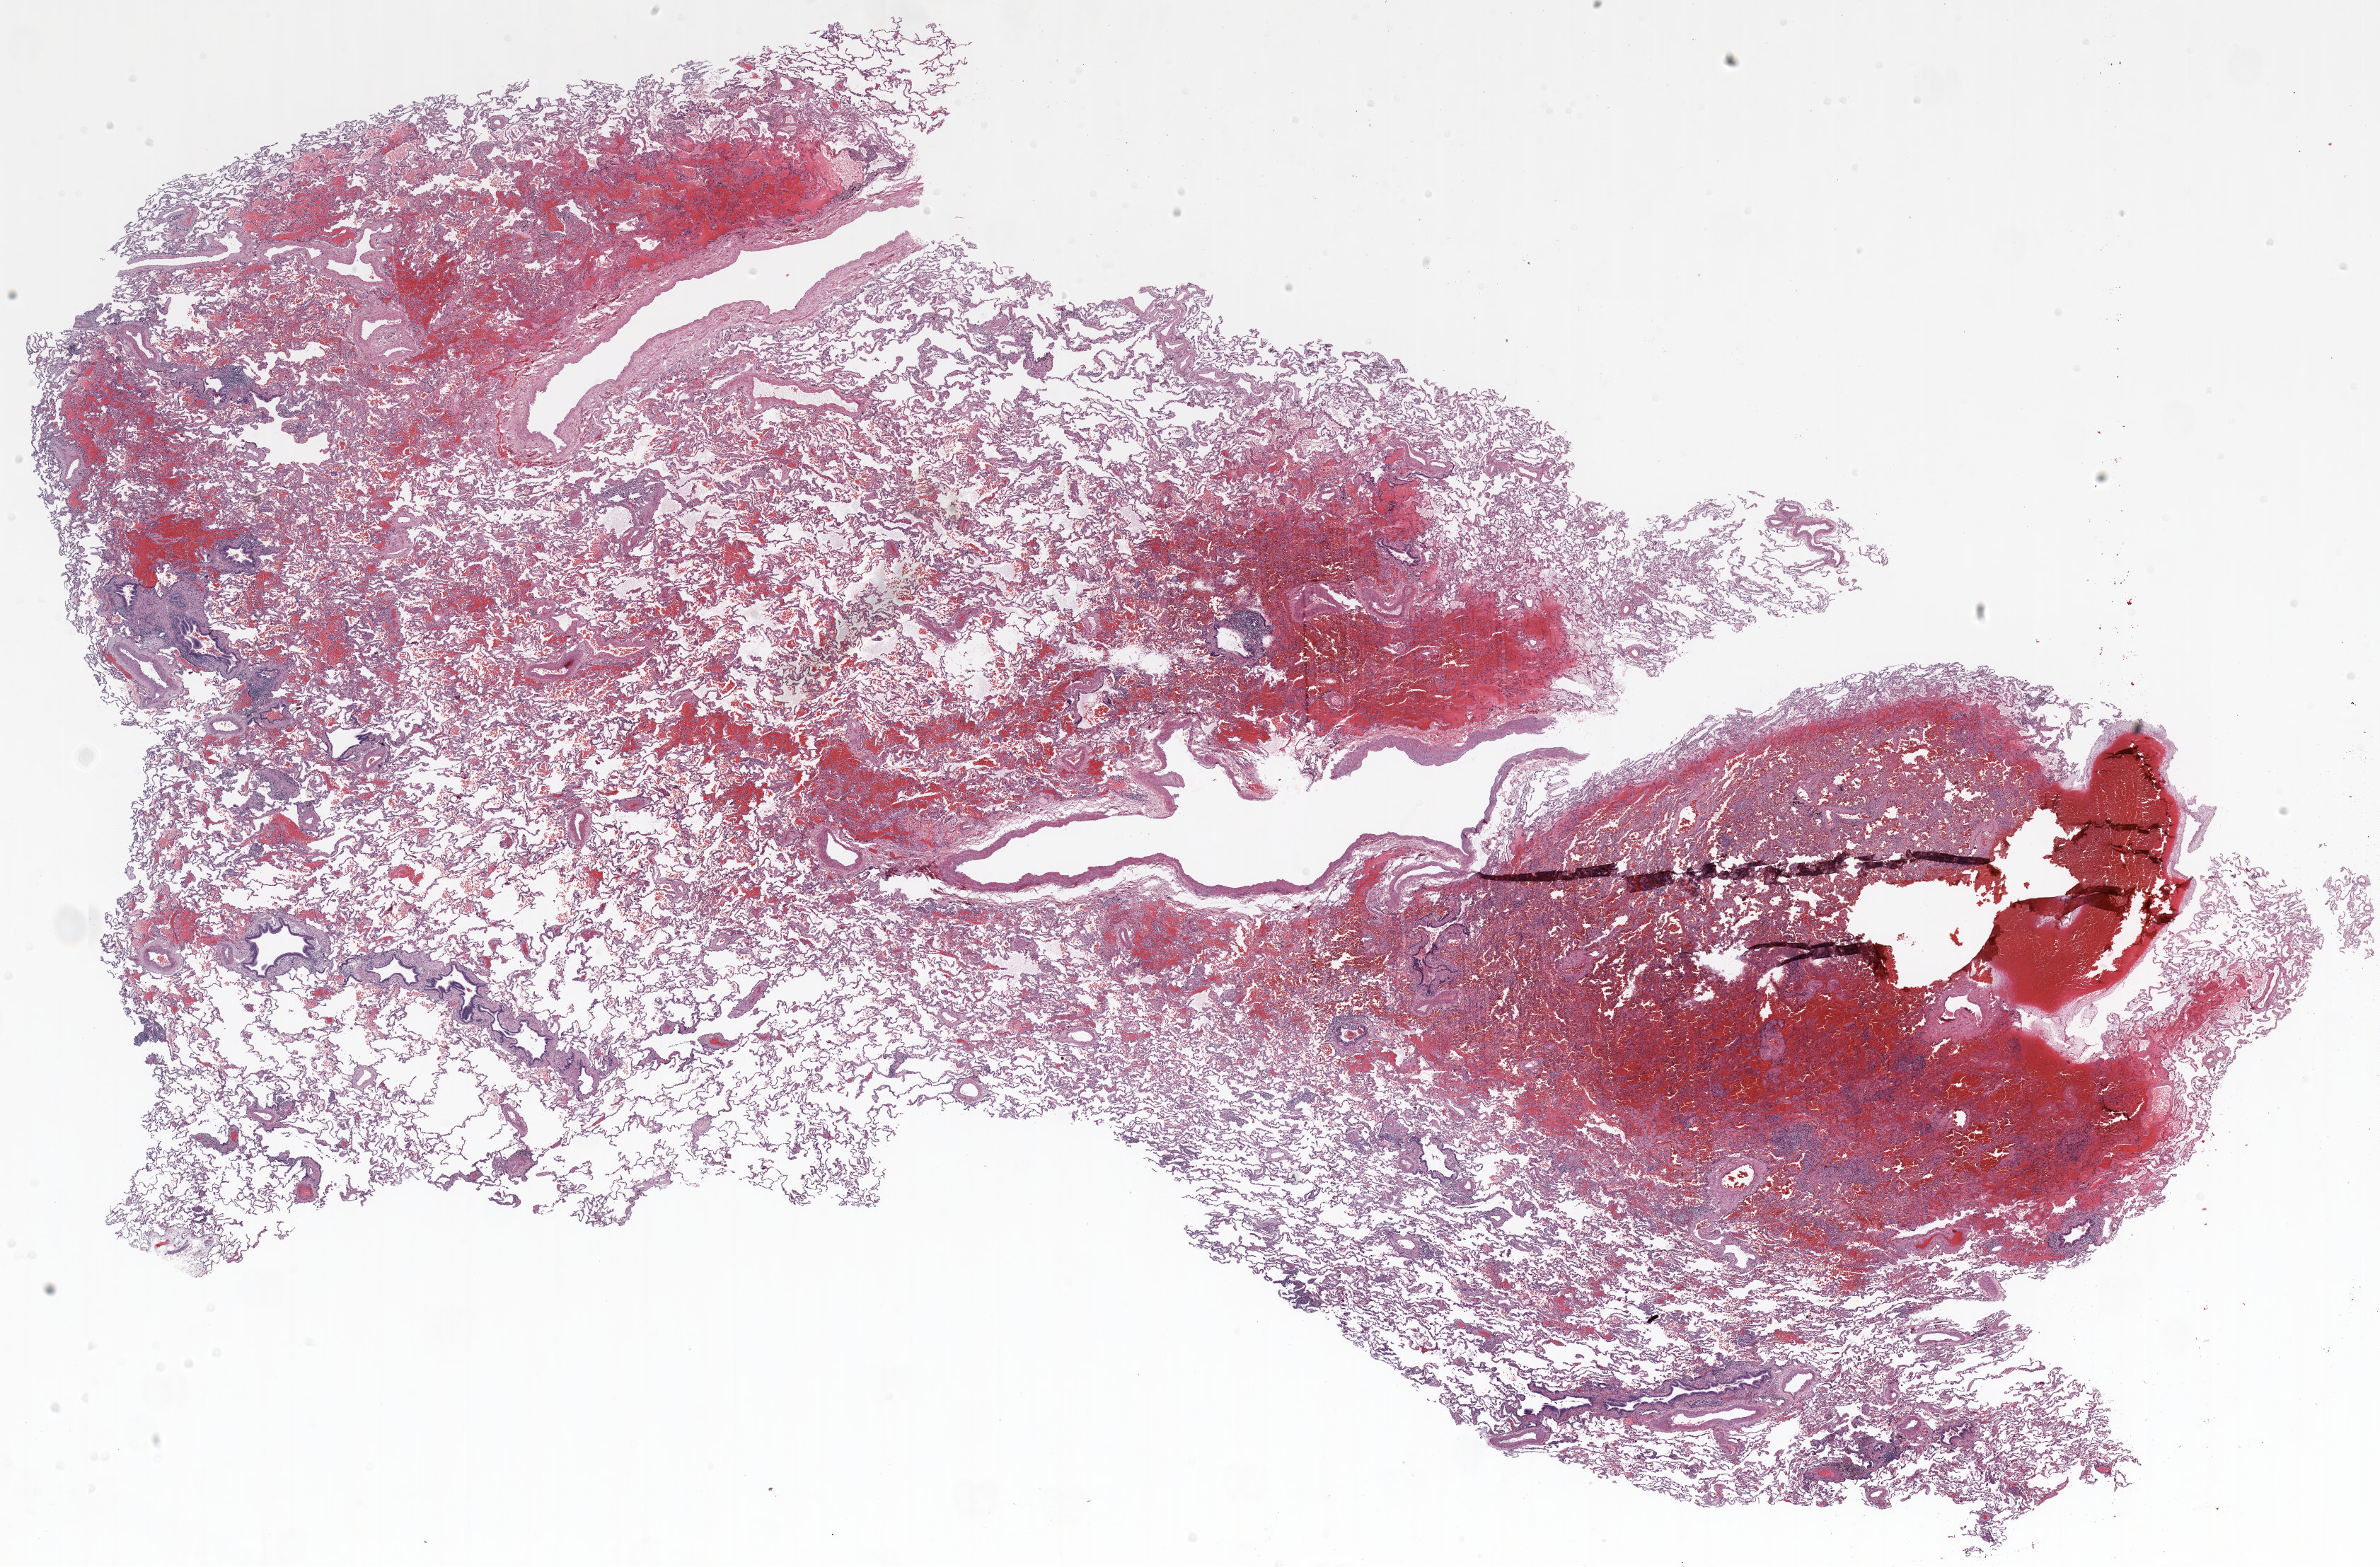
H&E whole-slide image — whole scanned area (about 27.0 x 17.8 mm, slide scanned at 20x) shown as a low-resolution overview. FFPE section. Lung tissue. Male, age 59 at enrolment. Grade: poorly differentiated (G3).
Primary tumour location (clinical record): left lower lobe. ICD-O-3 topography: lower lobe of lung (C34.3). Stage (AJCC 6th edition): IA. Participant's lung-cancer diagnosis: Large cell carcinoma, NOS (ICD-O-3 8012/3). Tumour size (pathology): 14 mm.